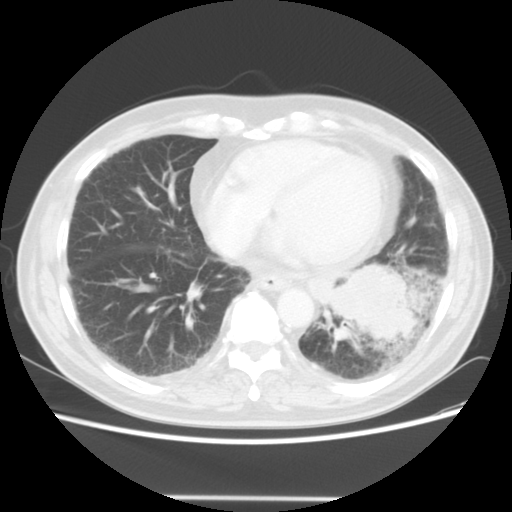
Chest CT, one axial slice; slice 16 of 56 in the series (ordered by position); reconstruction kernel STANDARD; 140 kVp; lung window (W 1500 / L -600 HU); 5 mm slice thickness; 512 × 512 image matrix. Male patient, age 66 years. From the clinical record (not read from this slice): clinical TNM (as recorded): T4 N3 M0; histopathological grade: G3.
Structures marked on this image (rectangle marked by the reading radiologist):
- lung tumour (recorded histology: small cell carcinoma): bounding box [x1, y1, x2, y2] px = [317, 260, 426, 345]